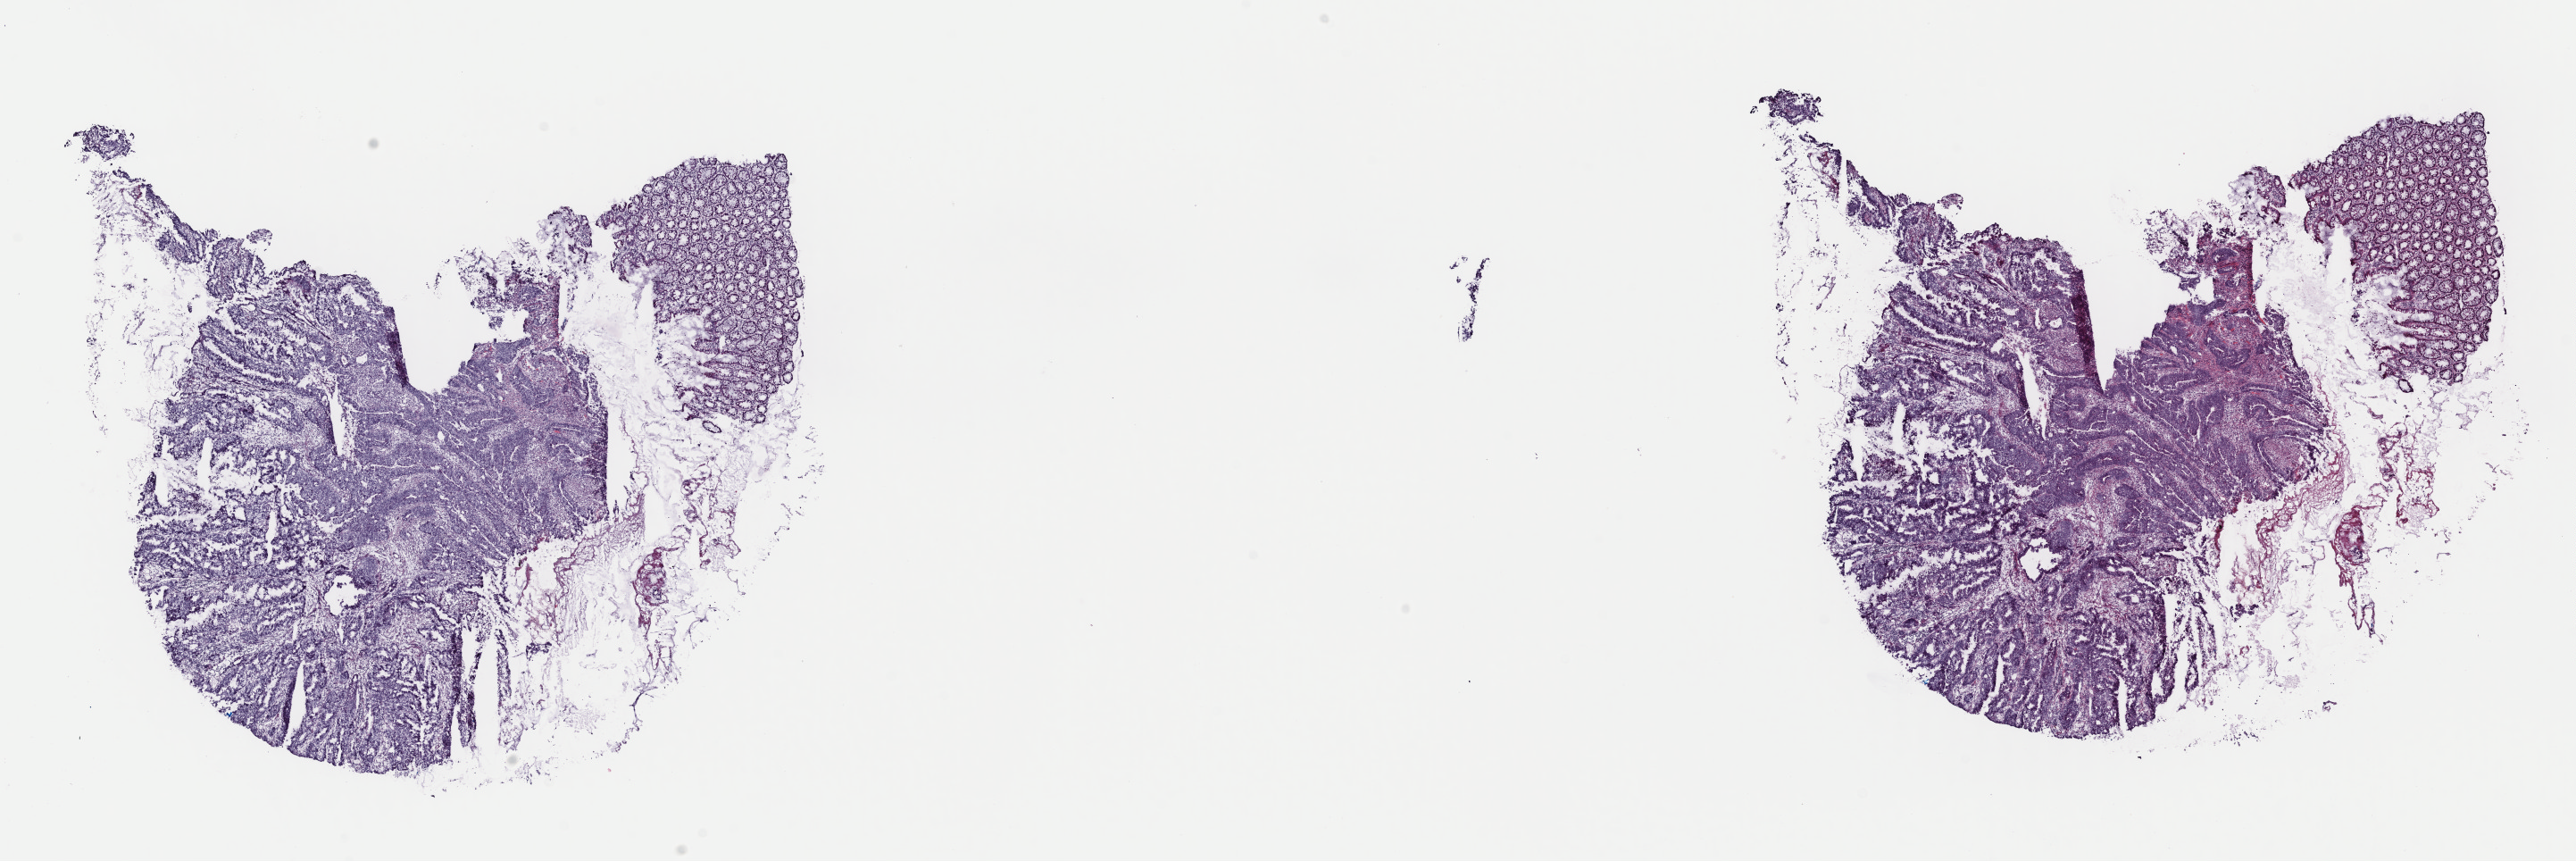
H&E whole-slide image, a low-resolution overview of the entire scanned area, about 22.8 x 7.6 mm (from a 40x scan). Frozen section from the top of the tissue portion. Sample: primary tumour, colon. Female, age 55 years at initial diagnosis. Pathologist review of this section (percent, as recorded): tumour cells 60%, tumour nuclei 60%, normal cells 15%, stromal cells 25%, necrosis 0%. Inflammatory infiltration, as recorded: lymphocyte infiltration 4%, monocyte infiltration 2%, neutrophil infiltration 5%.
AJCC pathologic stage: IIA (7th edition). Diagnosis: Adenocarcinoma, NOS (transverse colon). Lymph nodes positive (case pathology): 0 of 25 examined. TNM: T3 N0 M0.